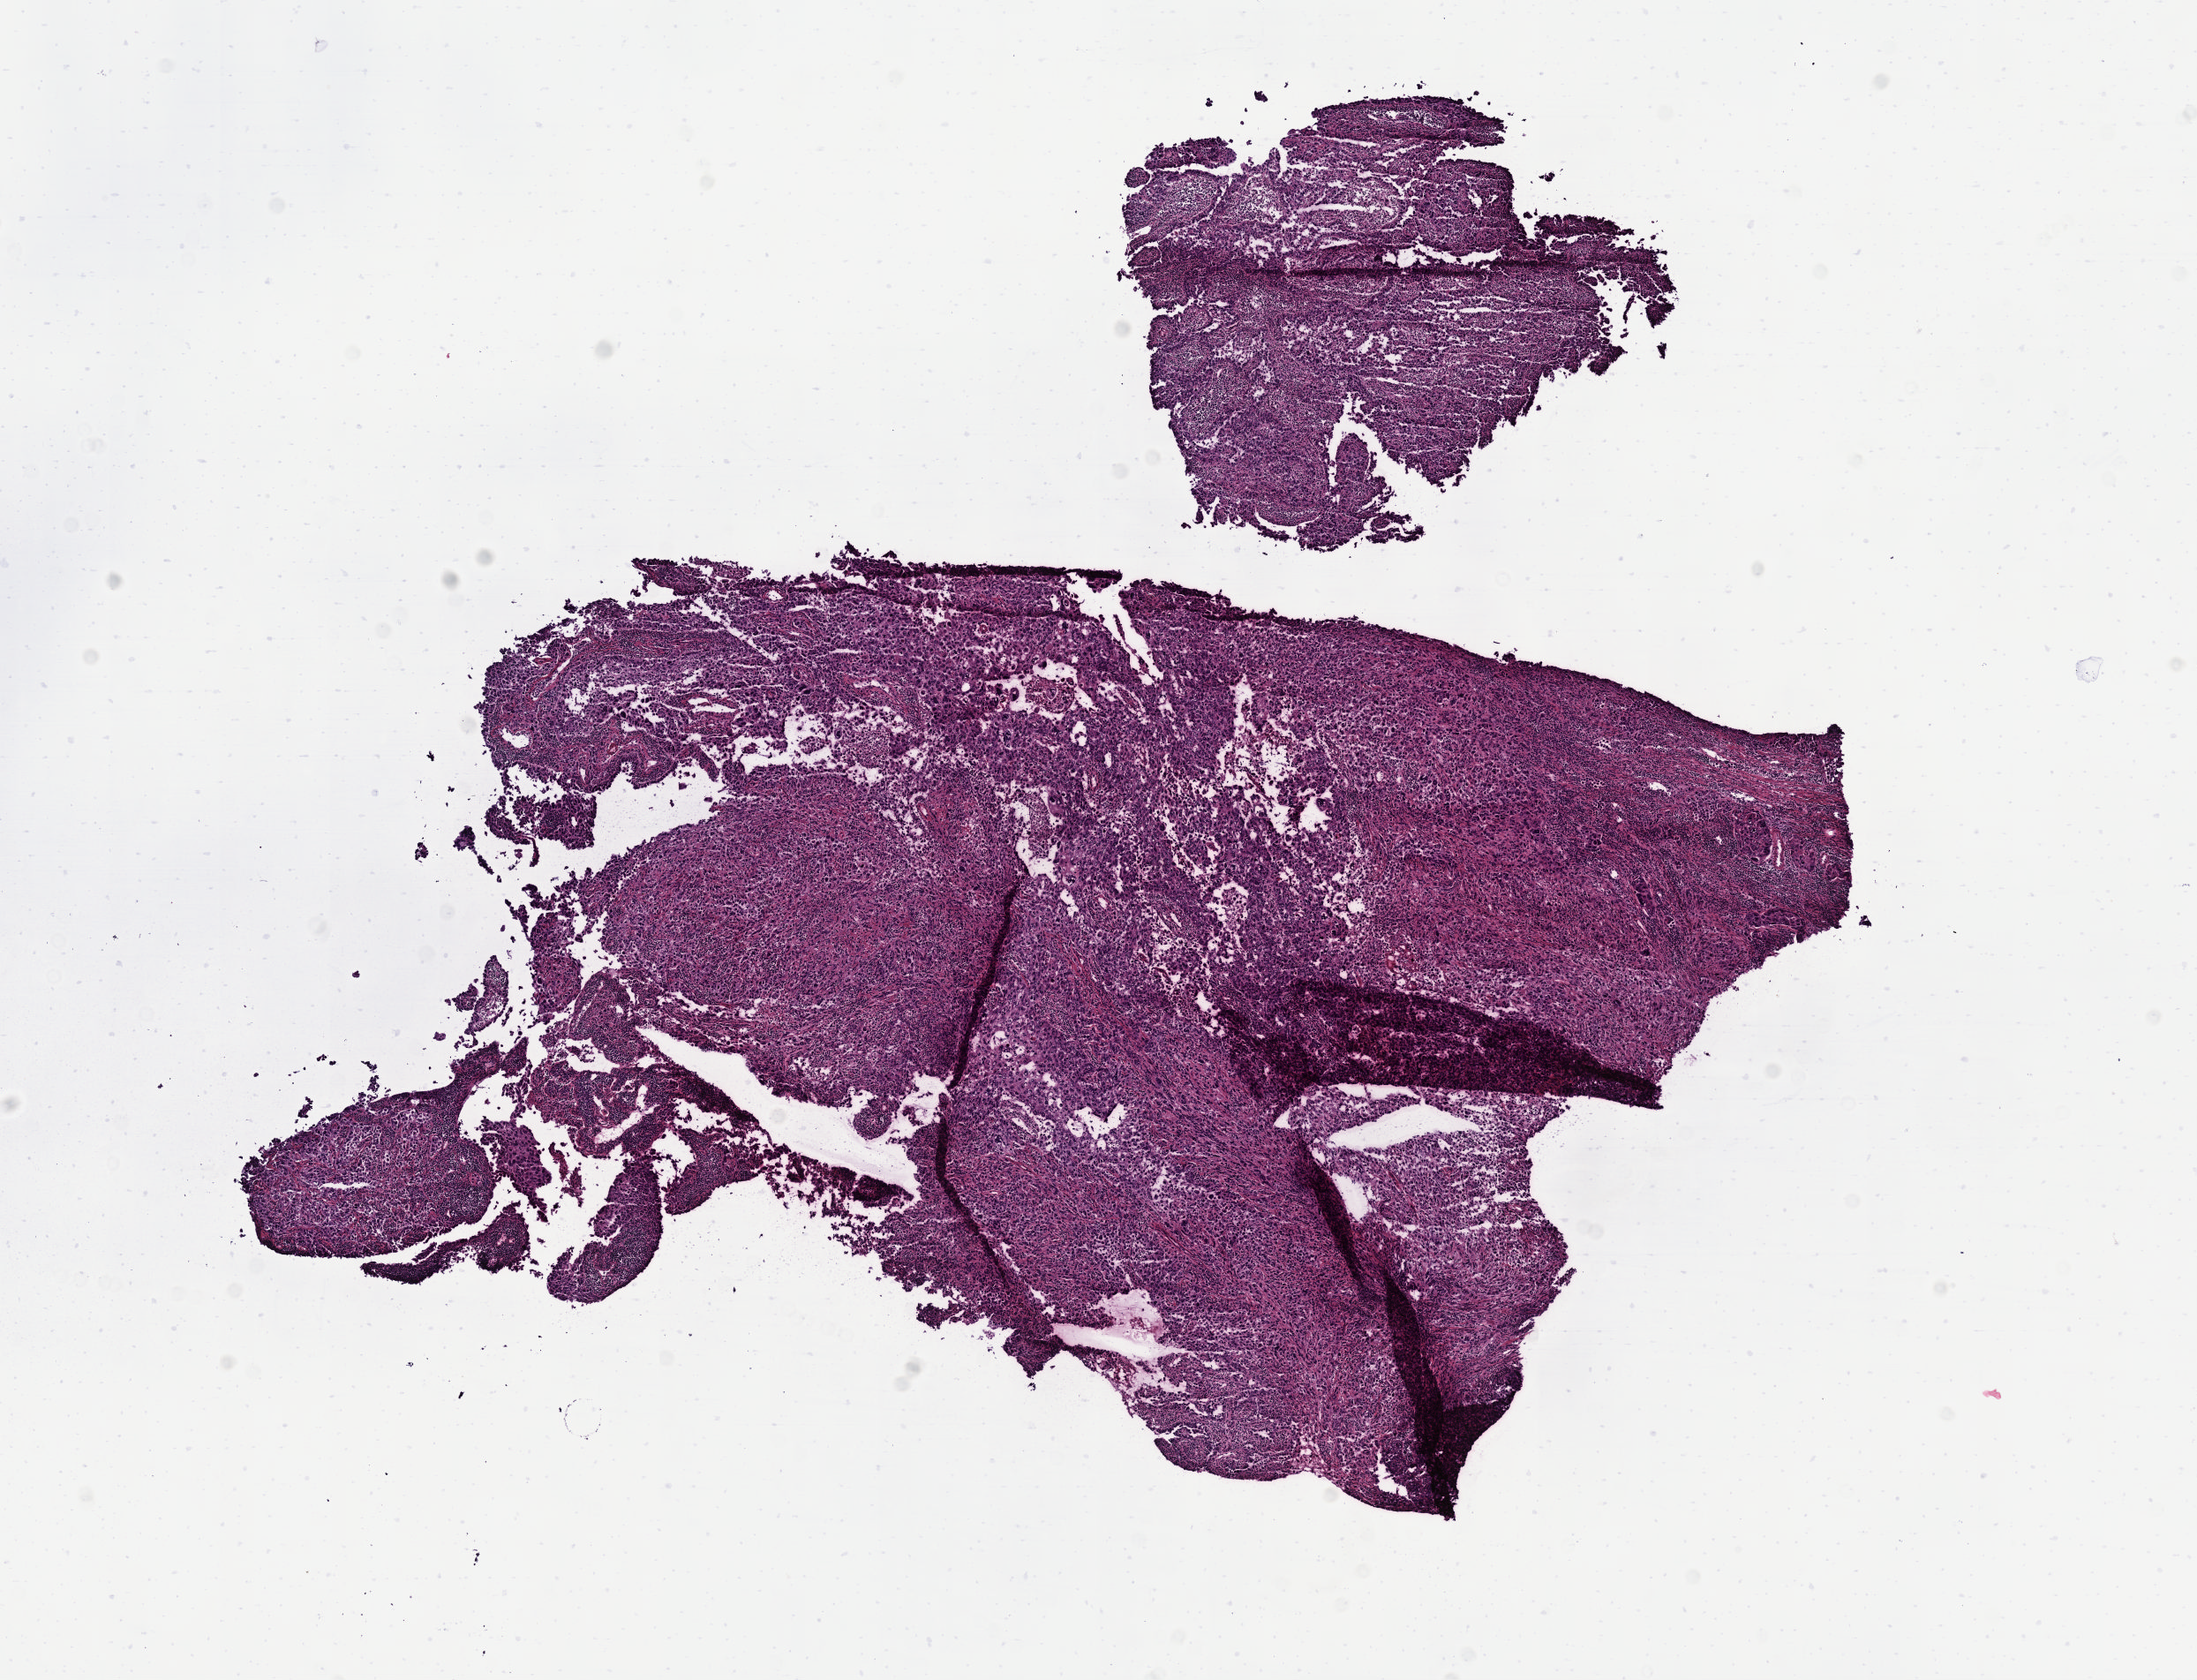
Digitized H&E-stained tissue section (whole slide) — a low-resolution overview of the entire scanned area, about 10.1 x 7.7 mm. Frozen section. Primary tumour sample from the uterus. Patient: female, age at initial diagnosis 61 years. Histologic grade: G3 (poorly differentiated). Composition of this section per pathologist review: tumour cells 70%, tumour nuclei 70%, normal cells 0%, stromal cells 25%, necrosis 5%. Infiltration values recorded for this section: lymphocyte infiltration 40%, monocyte infiltration 20%, neutrophil infiltration 20%.
- lymph nodes positive (case pathology): 0 of 2 examined
- FIGO stage: IIIC1
- diagnosis: Serous cystadenocarcinoma, NOS (endometrium)